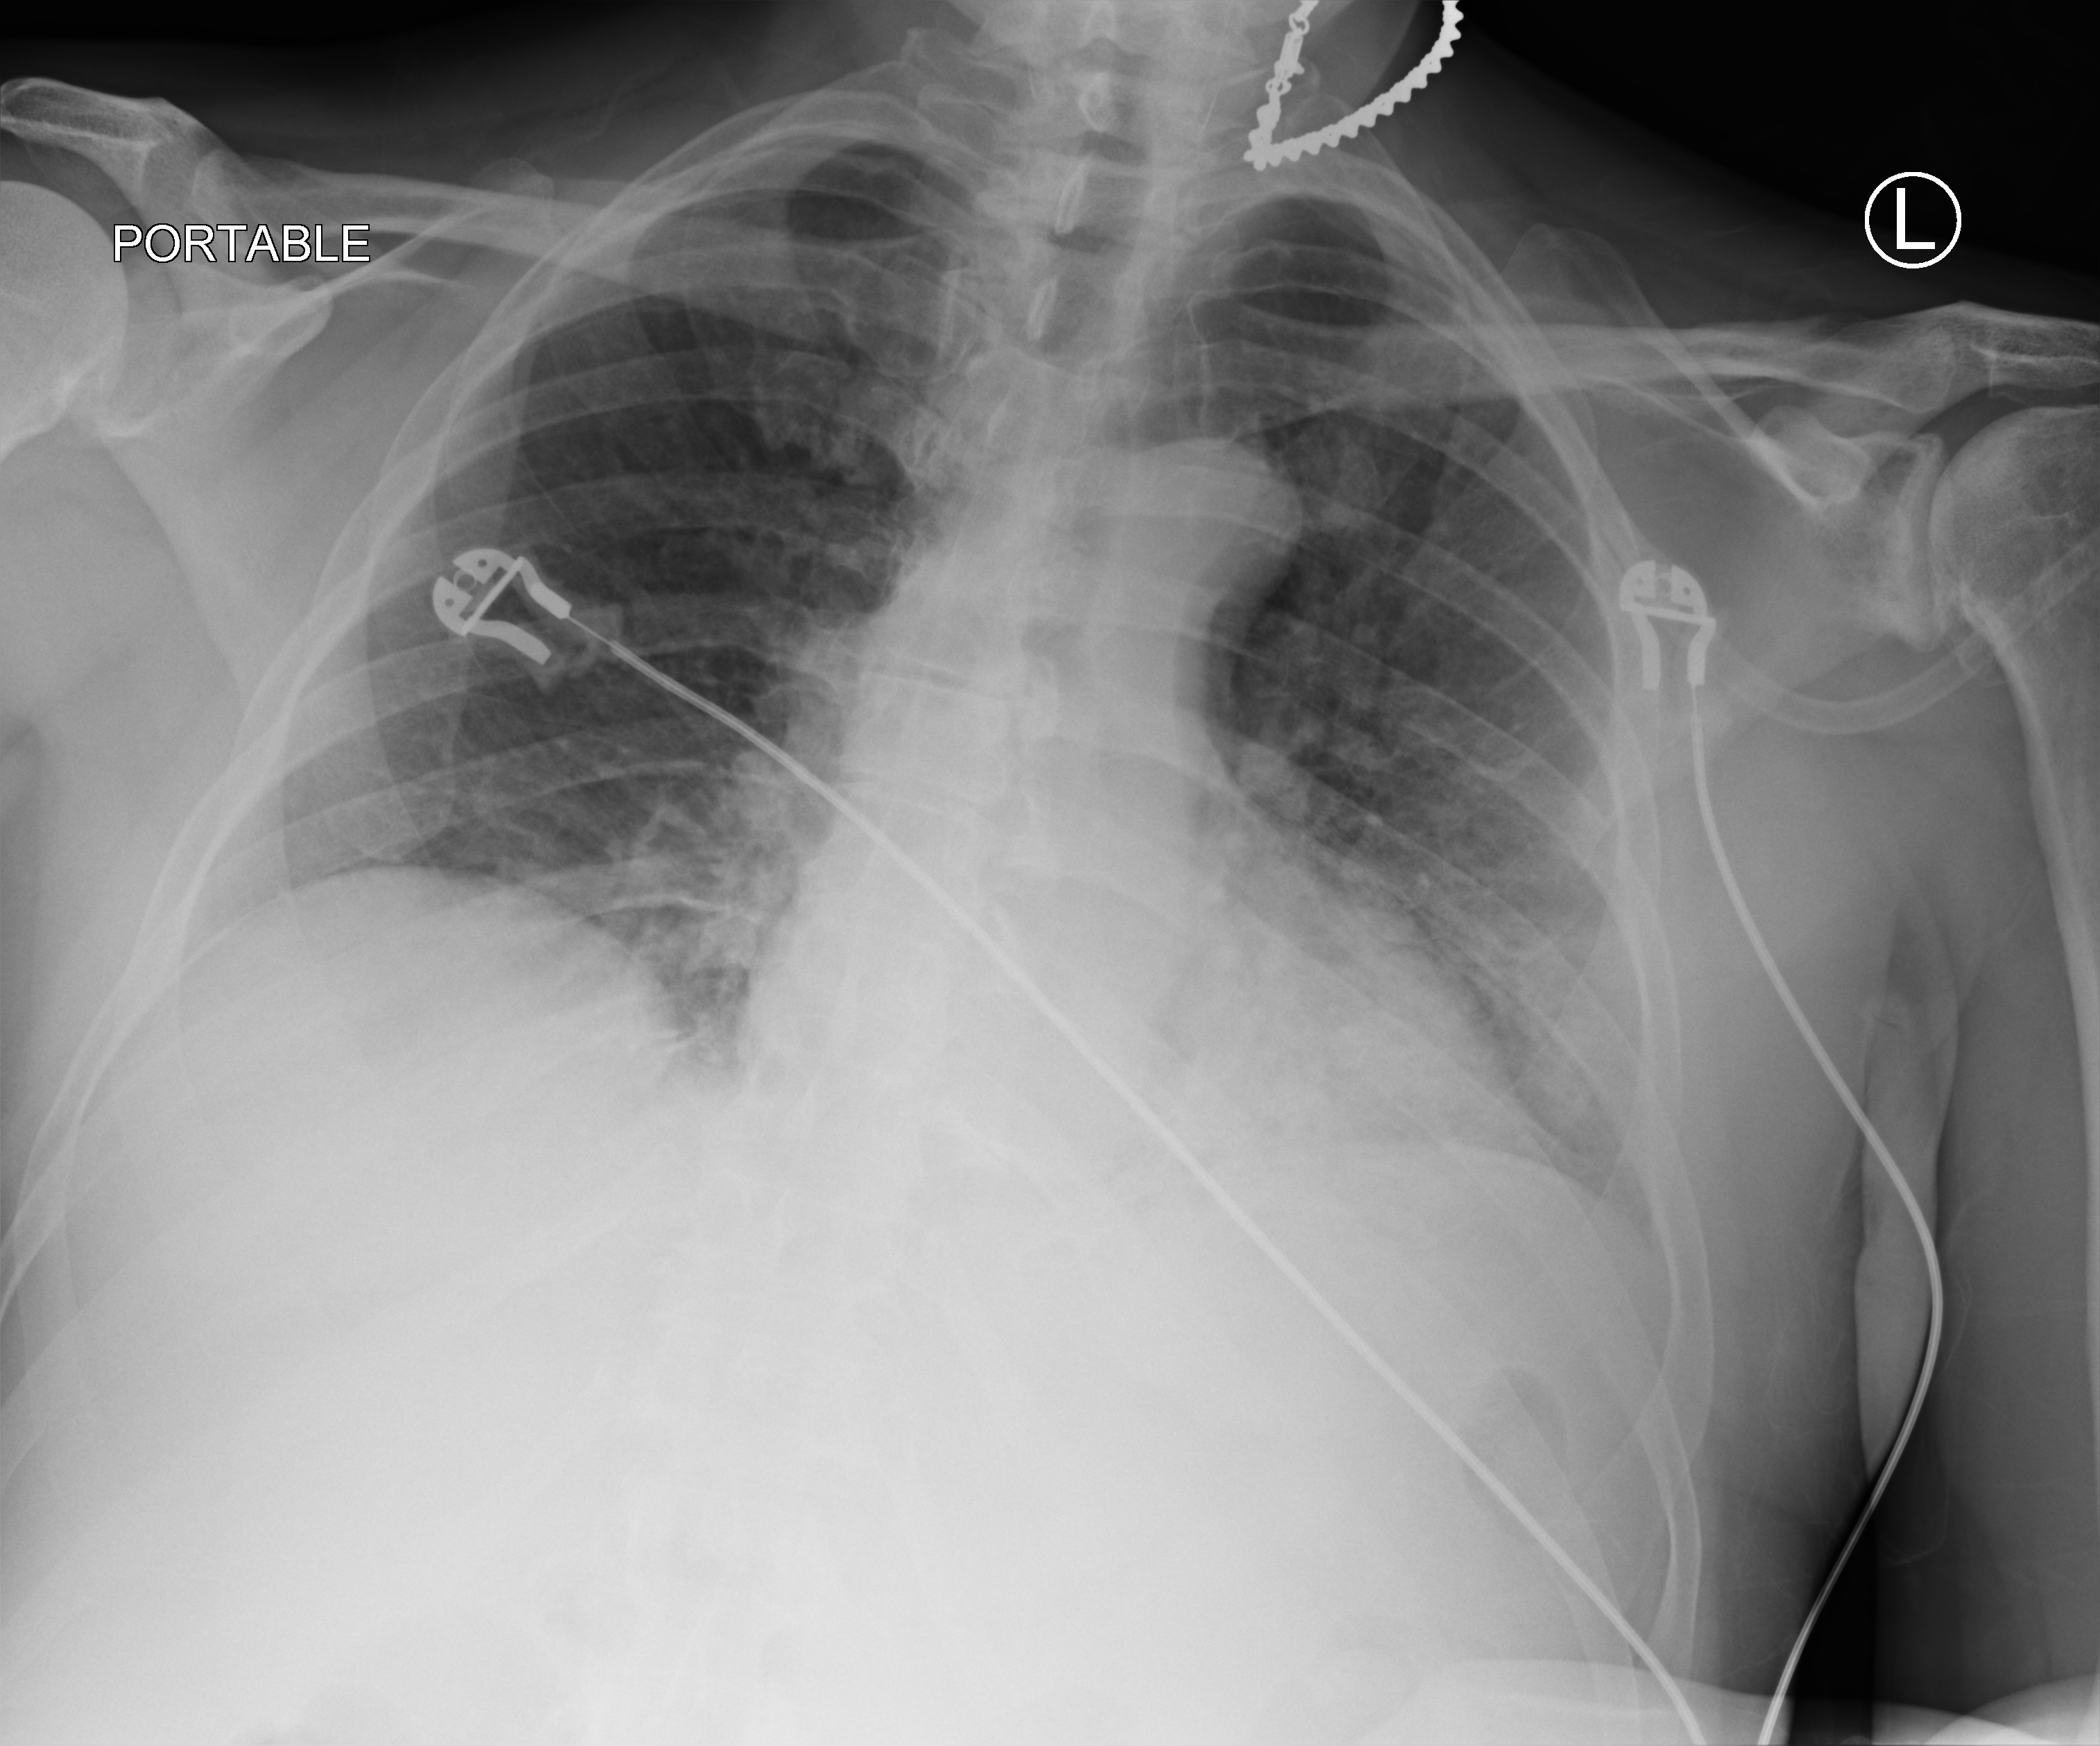
Bedside chest radiograph (computed radiography), anteroposterior (AP) projection. Male patient hospitalised with COVID-19, age 60–74 years.
Hospital-stay facts (about this admission, not read from this image; timing relative to this image not recorded):
- length of hospital stay: 6 days
- mechanically ventilated during this hospital stay: no
- admitted to intensive care during this hospital stay: no